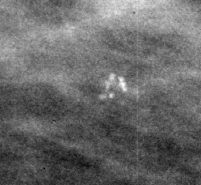
Cropped region of a digitized screen-film mammogram centred on a radiologist-marked abnormality, left breast, MLO view.
Marked abnormality: calcifications, morphology punctate / pleomorphic, distribution clustered; BI-RADS assessment category 4; subtlety rating 3 on a 1 (subtle) to 5 (obvious) scale; pathology (as recorded): benign.